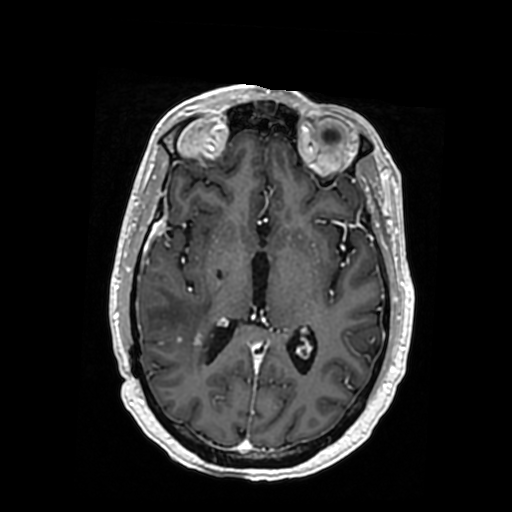
Brain MRI from a brain-tumour surgery series, one axial slice. Slice 185 of 364 in the series (ordered by position). T1-weighted post-contrast. 0.5 mm slice thickness. 512 × 512 image matrix, field of view 260 × 260 mm. Case-level facts recorded for this patient, not image findings: histopathology: Oligodendroglioma; WHO grade: 3; IDH mutation: yes.
Outlined on this slice (outlined manually by an expert reader):
- tumour: bounding box [x1, y1, x2, y2] px = [172, 331, 200, 342]